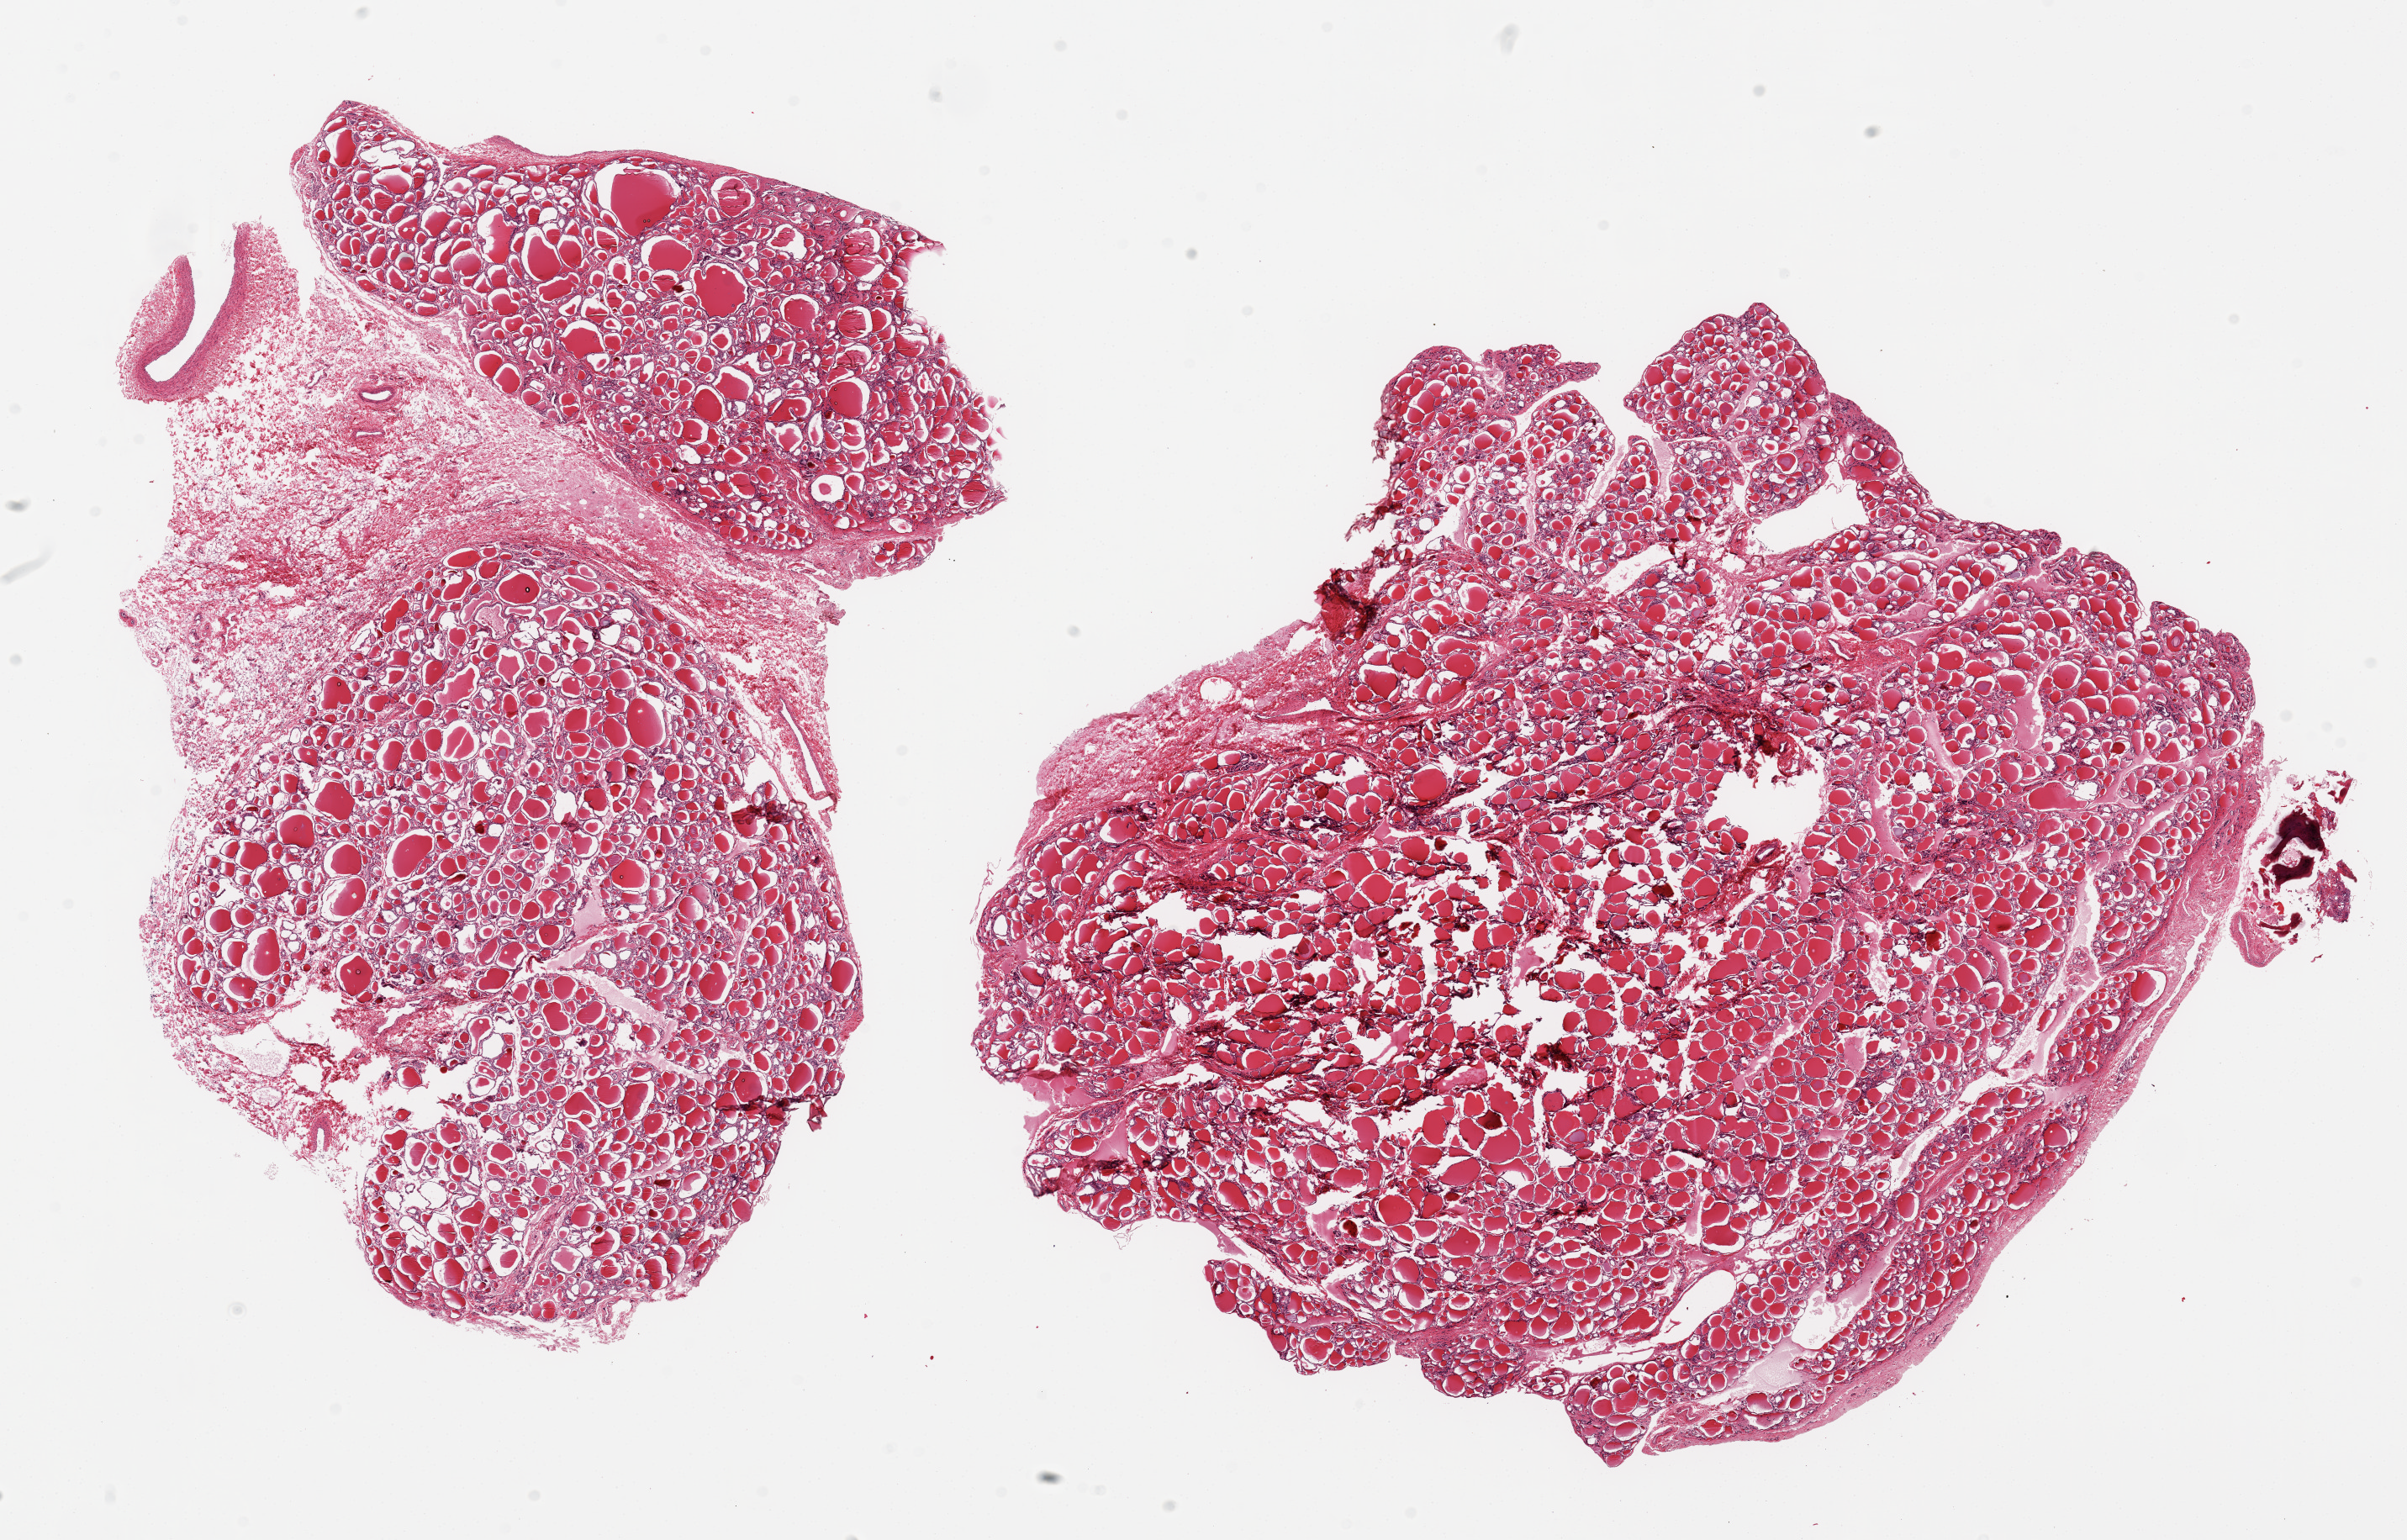
Hematoxylin and eosin (H&E) whole-slide image, brightfield — low-resolution overview of the scanned area, about 22.6 x 14.5 mm (slide scanned at 20x), PAXgene-fixed paraffin-embedded (PFPE) section, sampled site (target tissue): thyroid, donor tissue sample. Donor sex: female.
Reviewer comment on this tissue sample: 2 pieces; over-sized, one piece is ~30% fibrofatty tissue/vessels.